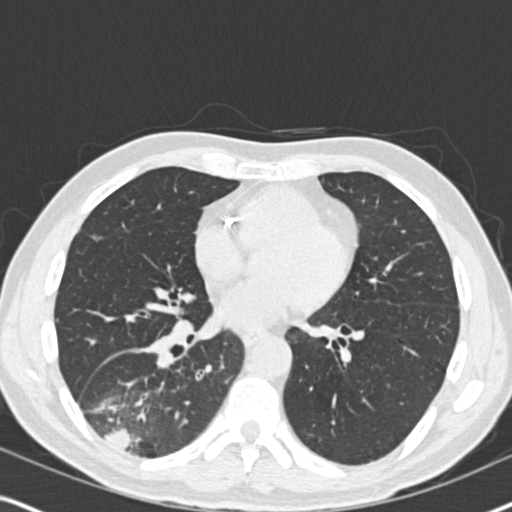
Chest CT (low-dose screening protocol), one axial image; second annual screen; lung window (W 1500 / L -600 HU); 2 mm slice thickness; slice 96 of 182 in the series. Male participant, aged 61 years at enrolment. Current smoker at enrolment.
Lesion marked by an expert reader, bounding box <65,350,195,470> (left, top, right, bottom; pixels). Screening reader's record for this exam (one nodule recorded; not confirmed to be the boxed lesion): non-calcified nodule or mass ≥4 mm, right lower lobe, 90 × 80 mm, soft tissue attenuation, pre-existing on the prior screen: yes; interval growth: yes. Official screen result: positive, other. Later outcome: lung cancer diagnosed 20 days after this screen — bronchiolo-alveolar adenocarcinoma, NOS, right lower lobe, moderately differentiated (G2), stage IIIB (AJCC 6th edition), 90 mm at pathology.